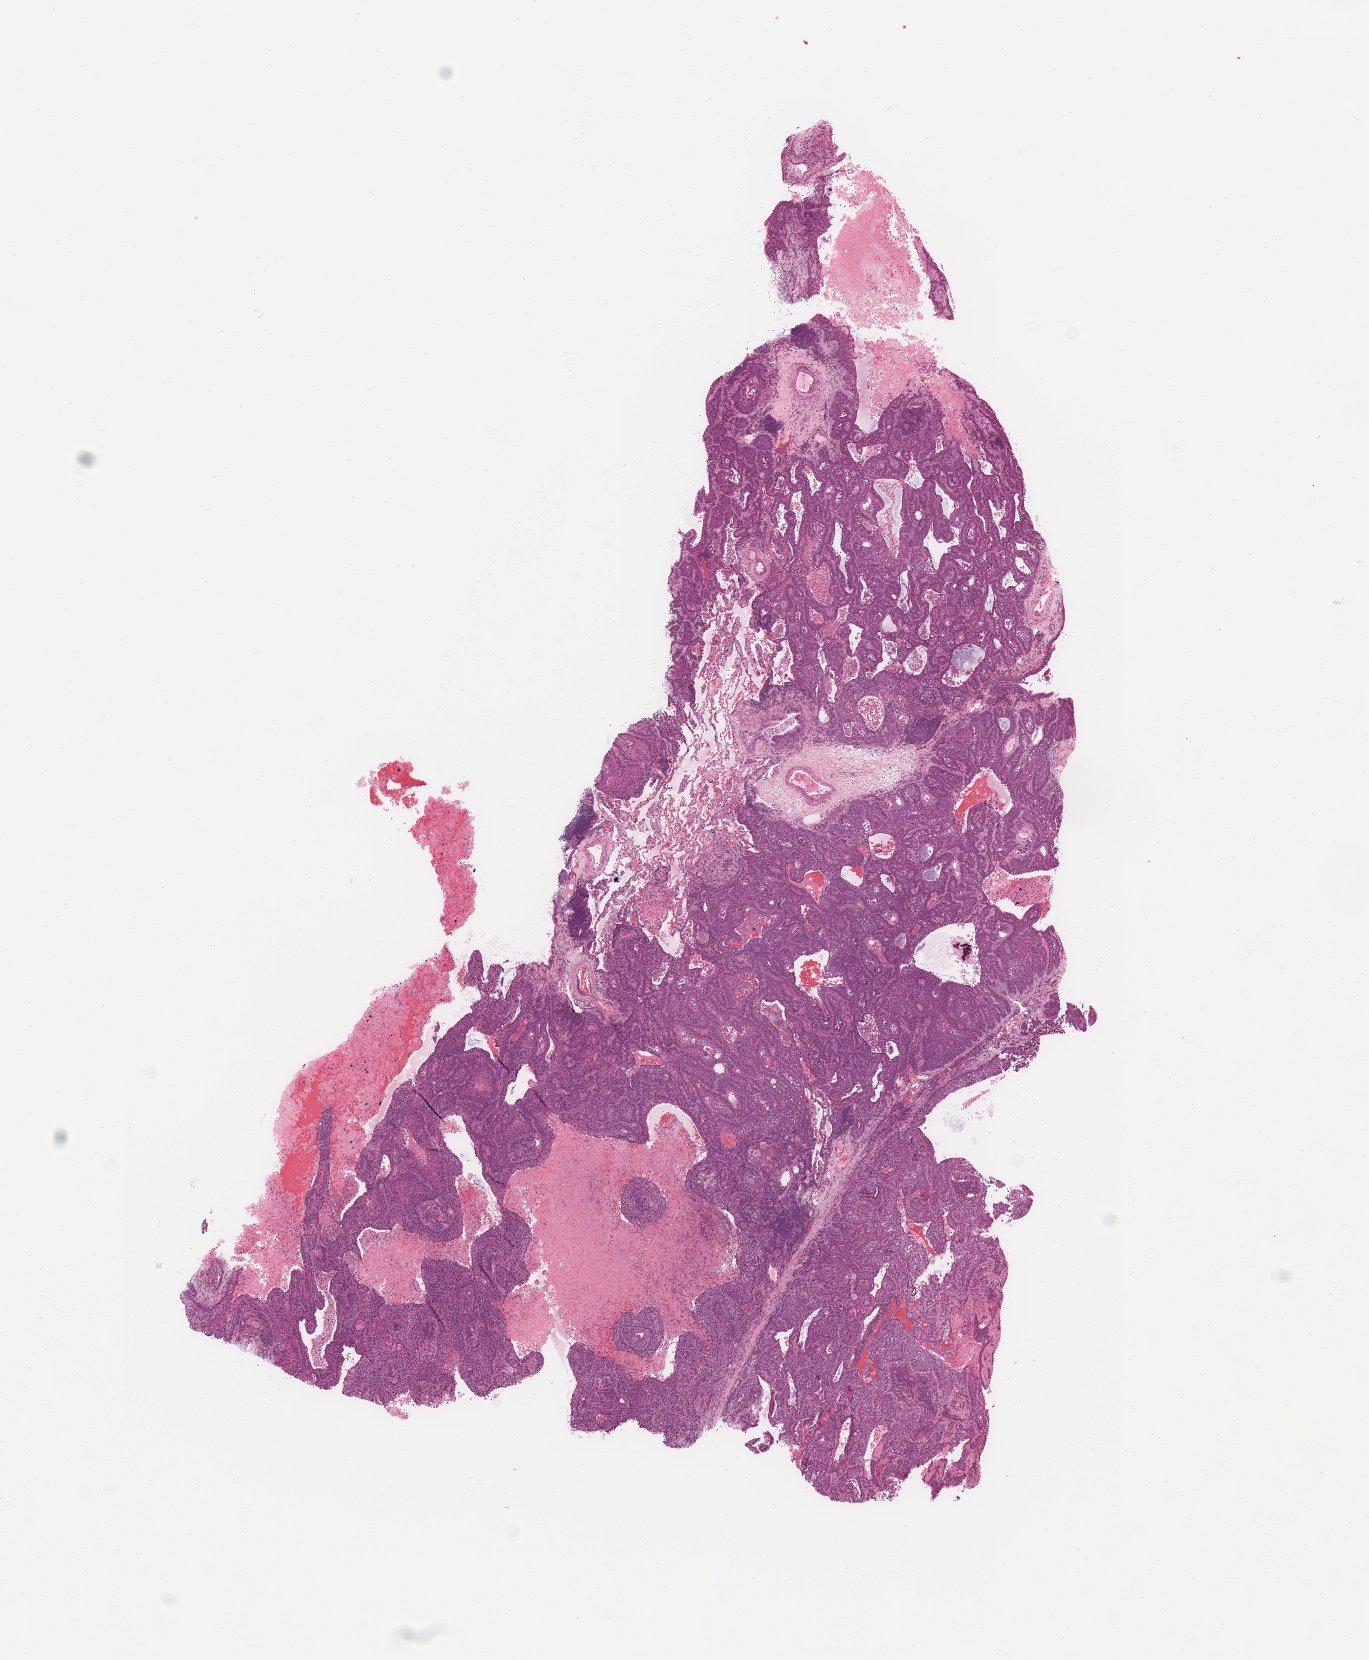
Whole-slide histology image, Hematoxylin and eosin (H&E) stained — a low-resolution overview of the entire scanned area, about 10.8 x 13.1 mm; tumour tissue sample, sampled site: lung. Male, 64 y/o. Histologic grade: G2 (moderately differentiated). Composition of this section per pathologist review: tumour nuclei 85%, necrosis 10%.
AJCC pathologic stage: IIB. Histologic diagnosis: Squamous cell carcinoma, NOS. Primary tumour site (as recorded): left upper lobe.